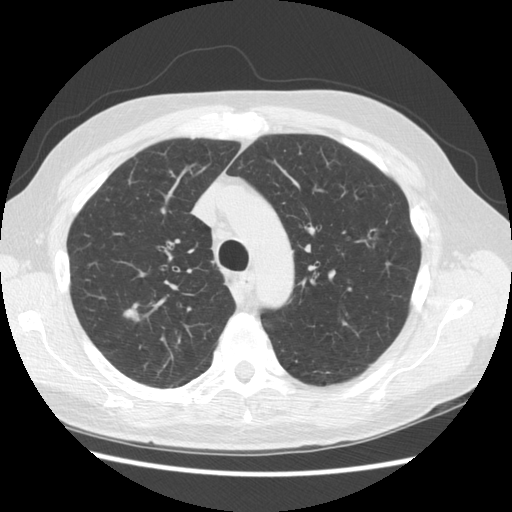
Low-dose screening chest CT, one axial slice; position 114 of 156 along the scan axis; reconstruction kernel STANDARD; lung window (W 1500 / L -600 HU); 512 × 512 image matrix, field of view 360 × 360 mm.
Annotated regions visible in this slice (expert manual segmentation):
- lesion 1 (tumor, upper lobe of right lung): bounding box [x1, y1, x2, y2] px = [123, 308, 140, 323]